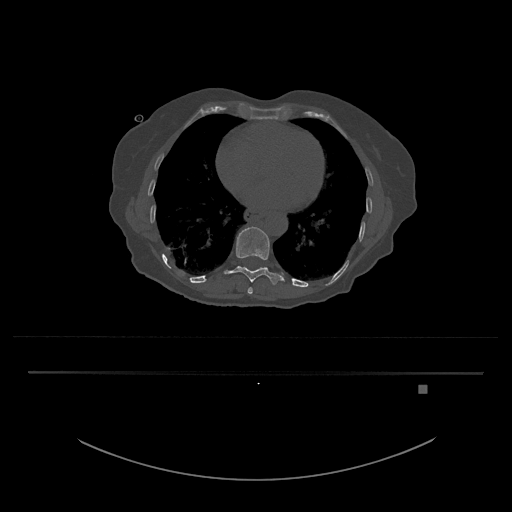
CT including the spine, one axial slice. Position 712 of 797 along the scan axis. Reconstruction kernel Br40s/3. 120 kVp. Bone window (W 1800 / L 400 HU). 0.5 mm slice thickness. 512 × 512 image matrix, field of view 500 × 500 mm. Female patient, age 57 years. From the clinical record (not read from this slice): primary cancer: cervical.
Outlined on this slice (semi-automatic segmentation, software-assisted and operator-edited):
- T10 vertebra: box from (x=224, y=227) to (x=284, y=285) px
- T9 vertebra: (x=247, y=287)–(x=253, y=294)